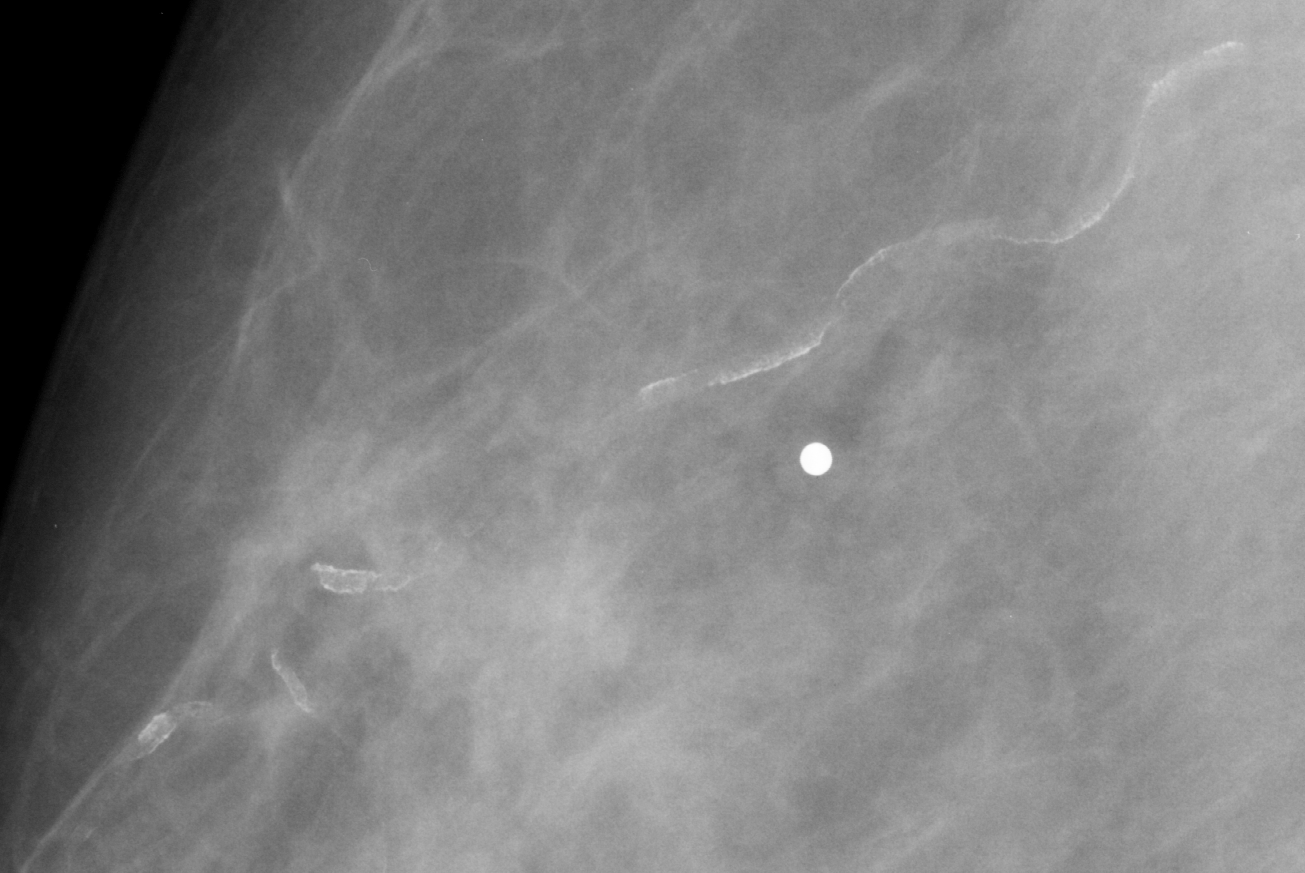
Cropped region of a digitized screen-film mammogram centred on a radiologist-marked abnormality; right breast; MLO view; BI-RADS breast density category 2 (scale 1–4).
- Marked abnormality: calcifications, morphology vascular; BI-RADS assessment category 2; benign; no additional work-up was recommended (benign without callback).